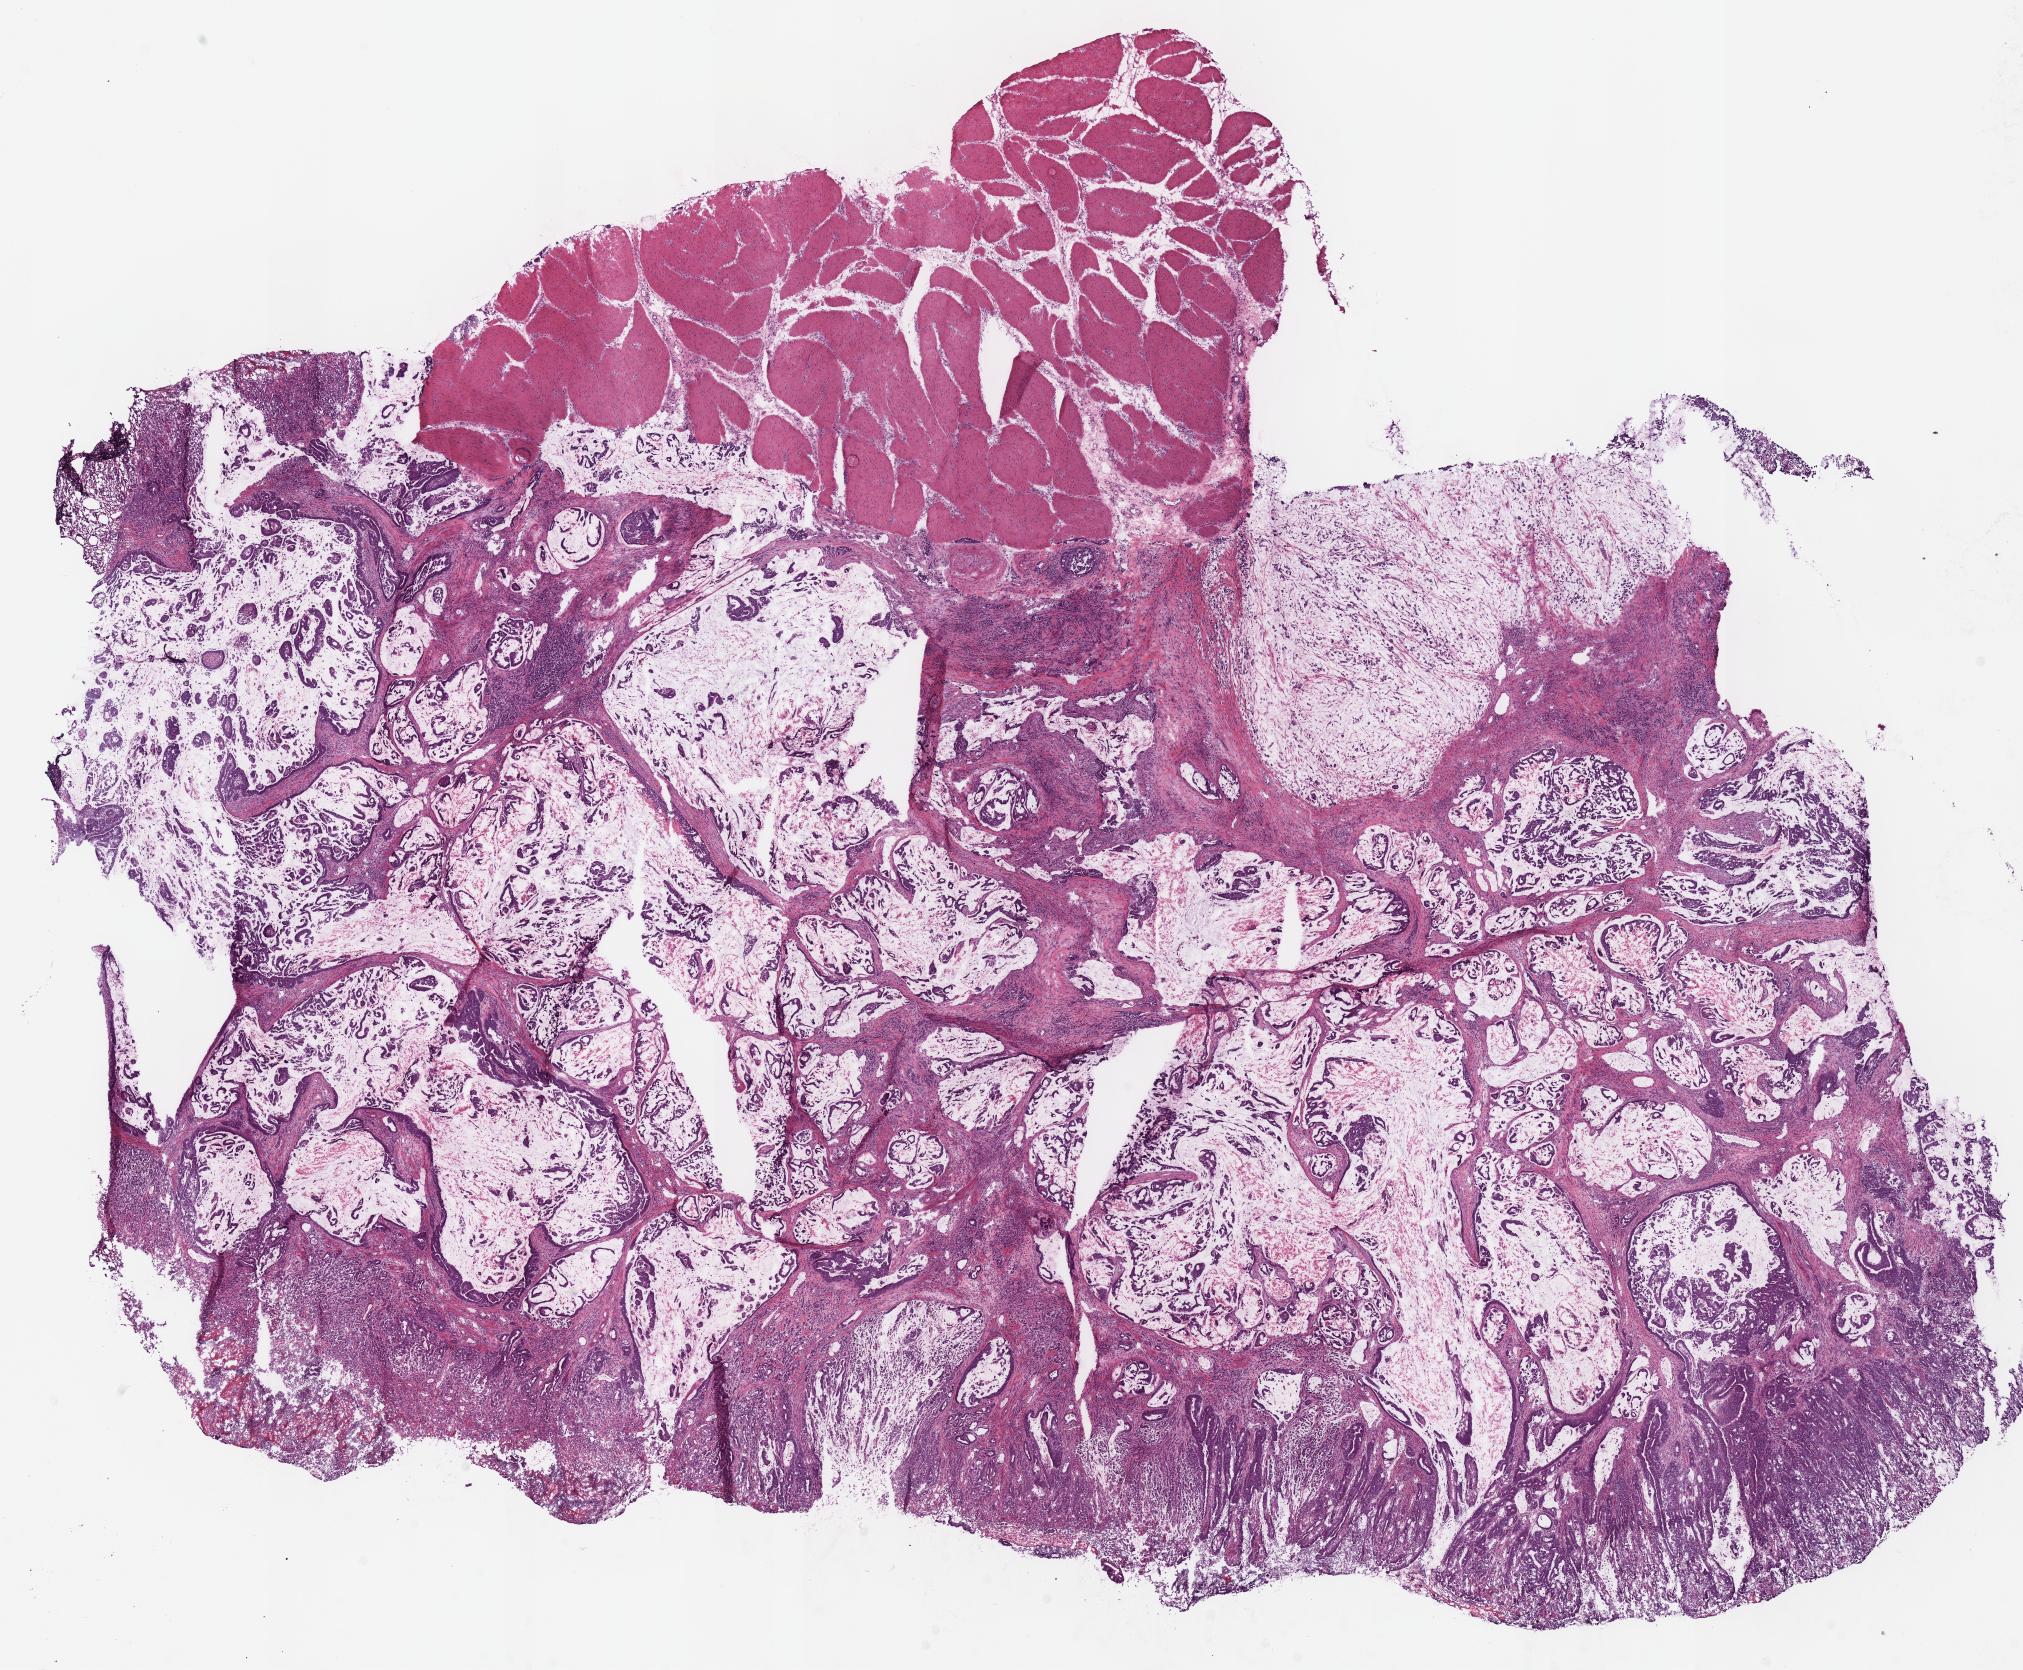
H&E-stained whole-slide image, a low-resolution overview of the entire scanned area, about 15.9 x 13.2 mm (acquisition: 40x scan). Frozen section. Primary tumour sample from the stomach. Female patient; age at initial diagnosis 63 years. Histologic grade: G2 (moderately differentiated). Pathologist review of this section (percent, as recorded): tumour cells 68%, tumour nuclei 65%, normal cells 17%, stromal cells 0%, necrosis 15%. Infiltration values recorded for this section: lymphocyte infiltration 10%, monocyte infiltration 0%, neutrophil infiltration 20%.
AJCC pathologic stage: IB. Diagnosis: Adenocarcinoma, NOS (fundus of stomach).